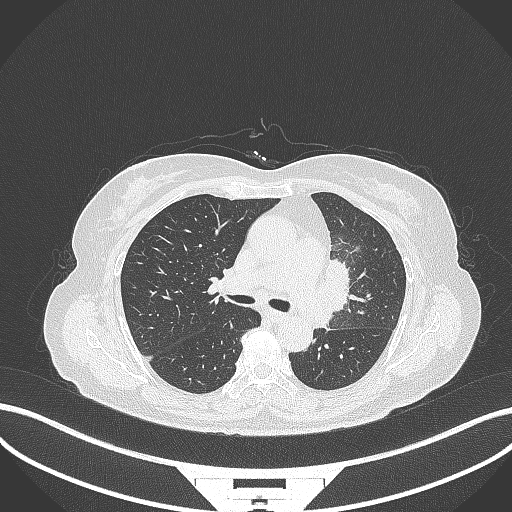
Chest CT, one axial slice. Position 206 of 382 along the scan axis. Reconstruction kernel B70f. Lung window (W 1500 / L -600 HU). 512 × 512 image matrix, field of view 400 × 400 mm. Female patient, age 64 years. From the clinical record (not read from this slice): clinical TNM (as recorded): T2a N2 M0.
Annotated regions visible in this slice (rectangle marked by the reading radiologist):
- lung tumour (recorded histology: adenocarcinoma): bounding box [x1, y1, x2, y2] px = [317, 258, 355, 314]